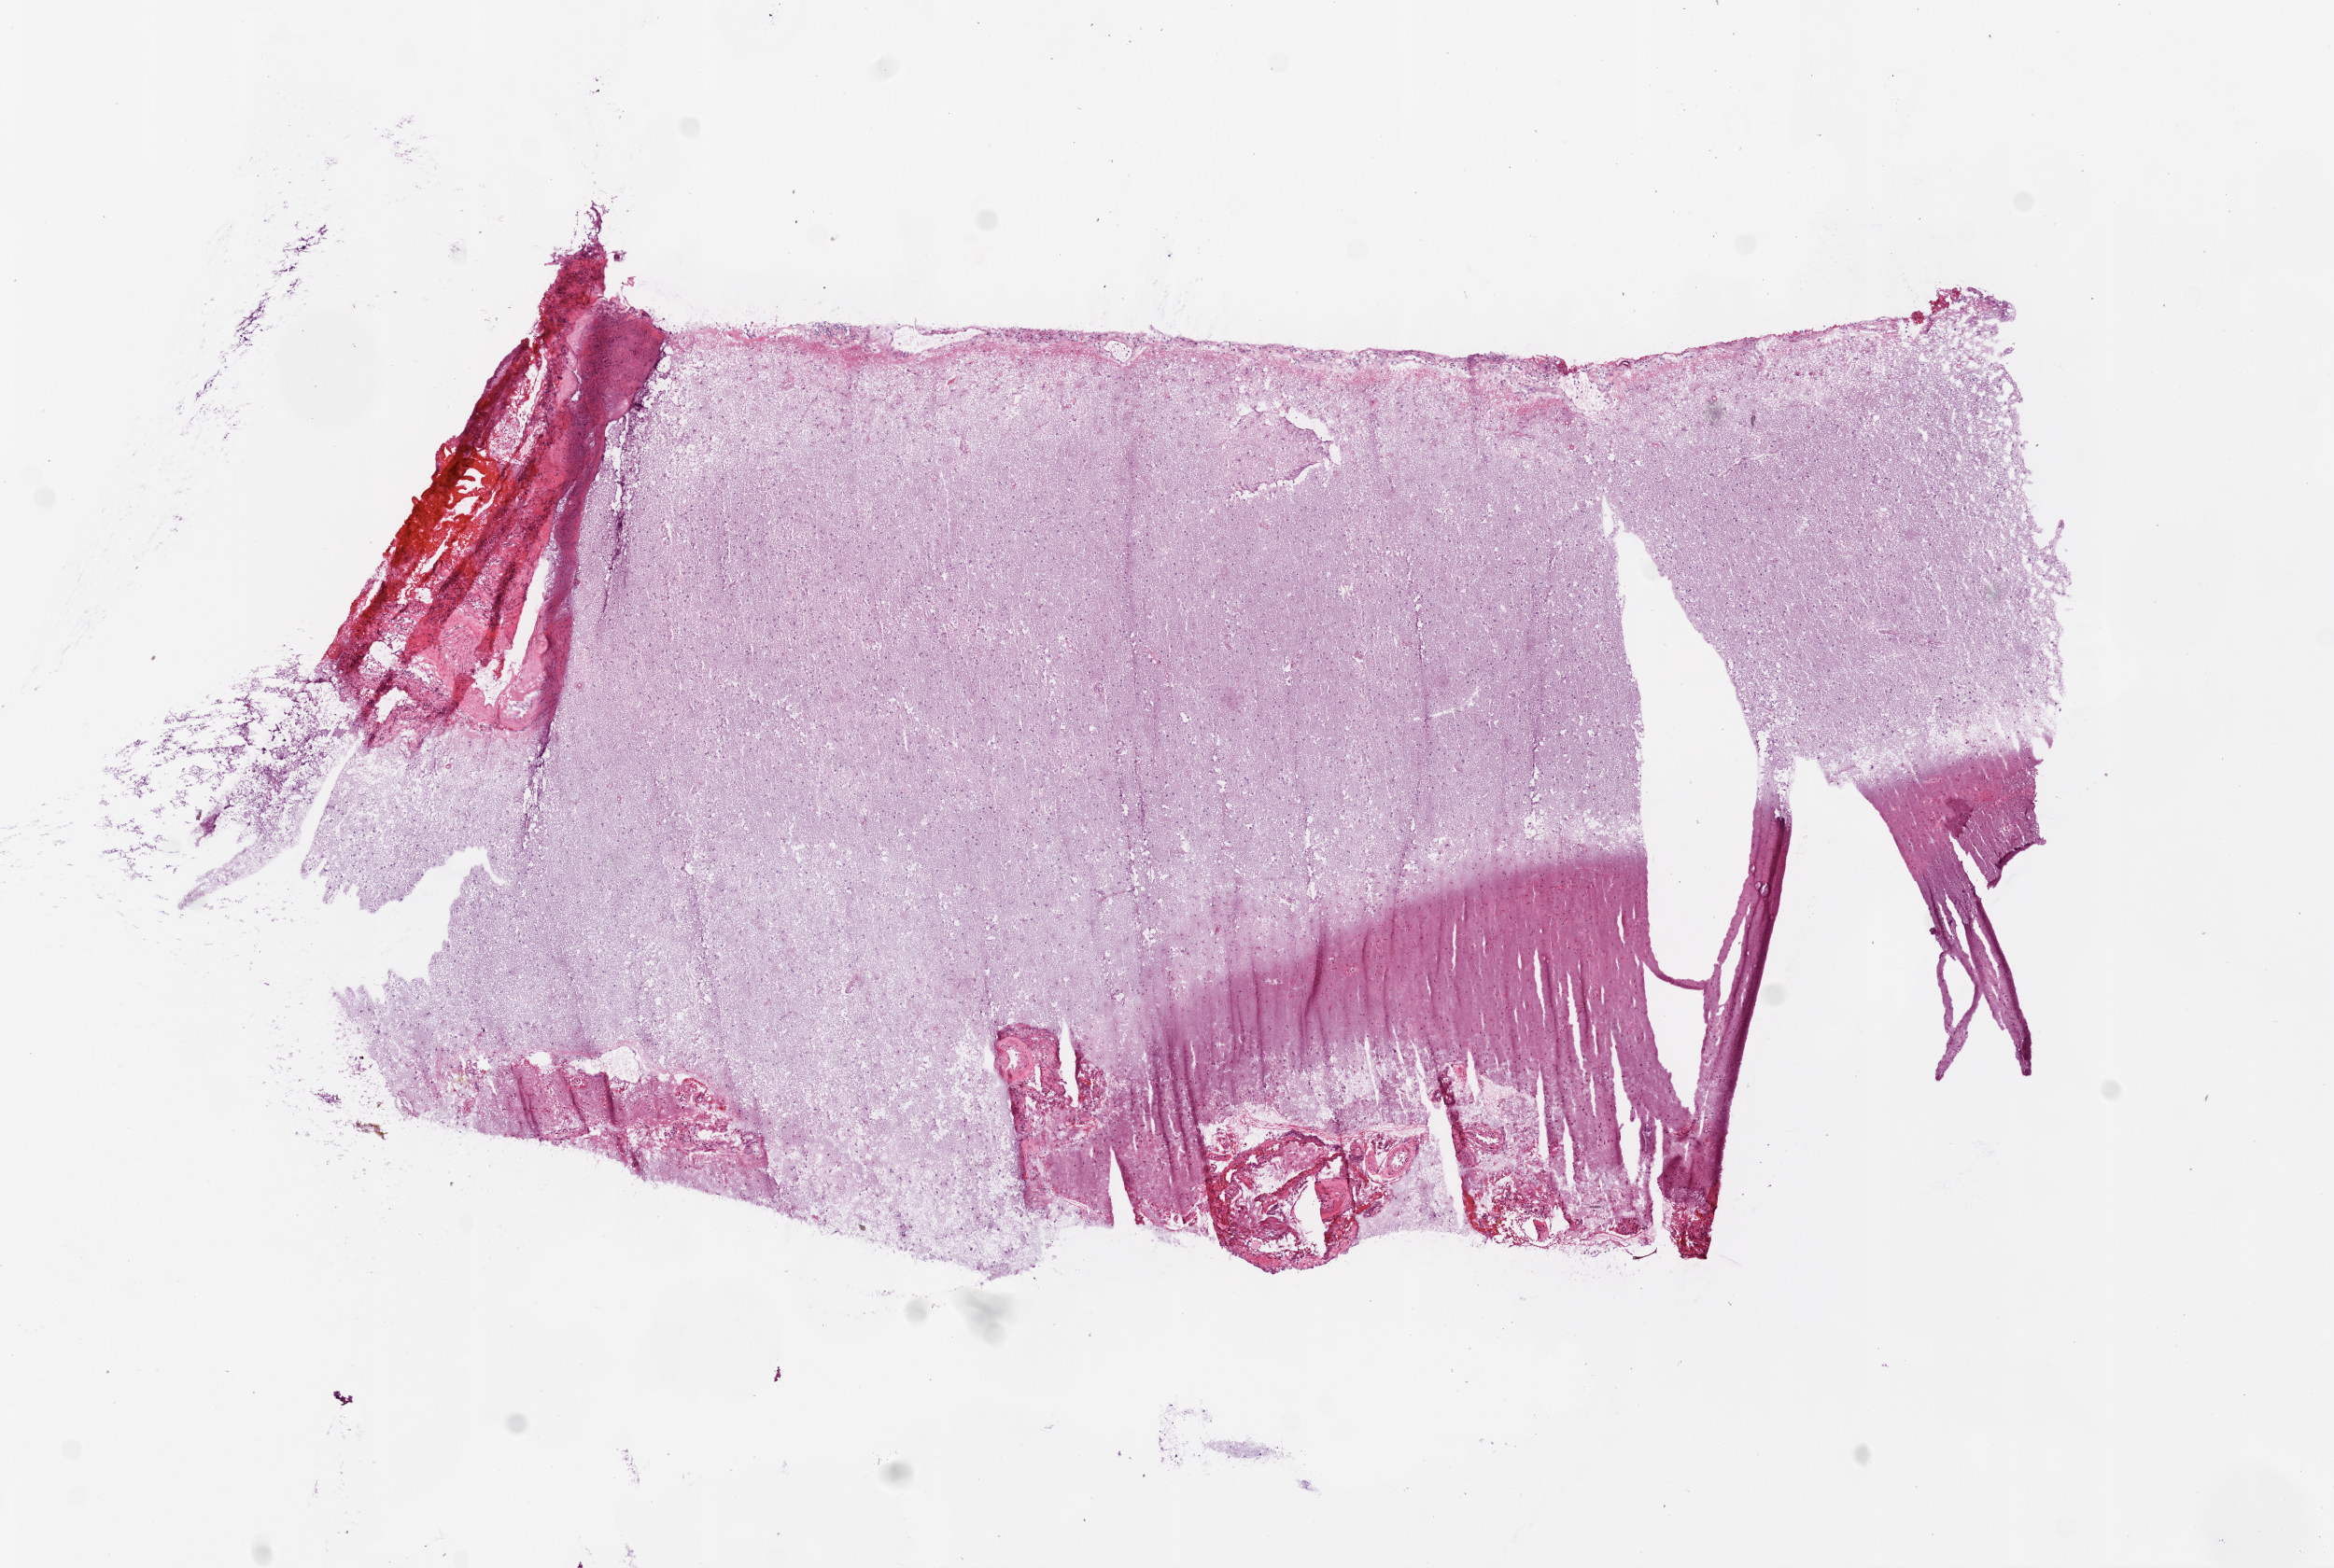
Digitized H&E-stained tissue section (whole slide), whole scanned area (about 10.0 x 6.7 mm) shown as a low-resolution overview; frozen section from the bottom of the tissue portion; primary tumour sample from the brain. Male patient; age at initial diagnosis 72 years. Composition of this section per pathologist review: tumour cells 0%, tumour nuclei 0%, normal cells 95%, stromal cells 5%, necrosis 0%.
Histologic diagnosis: Glioblastoma.